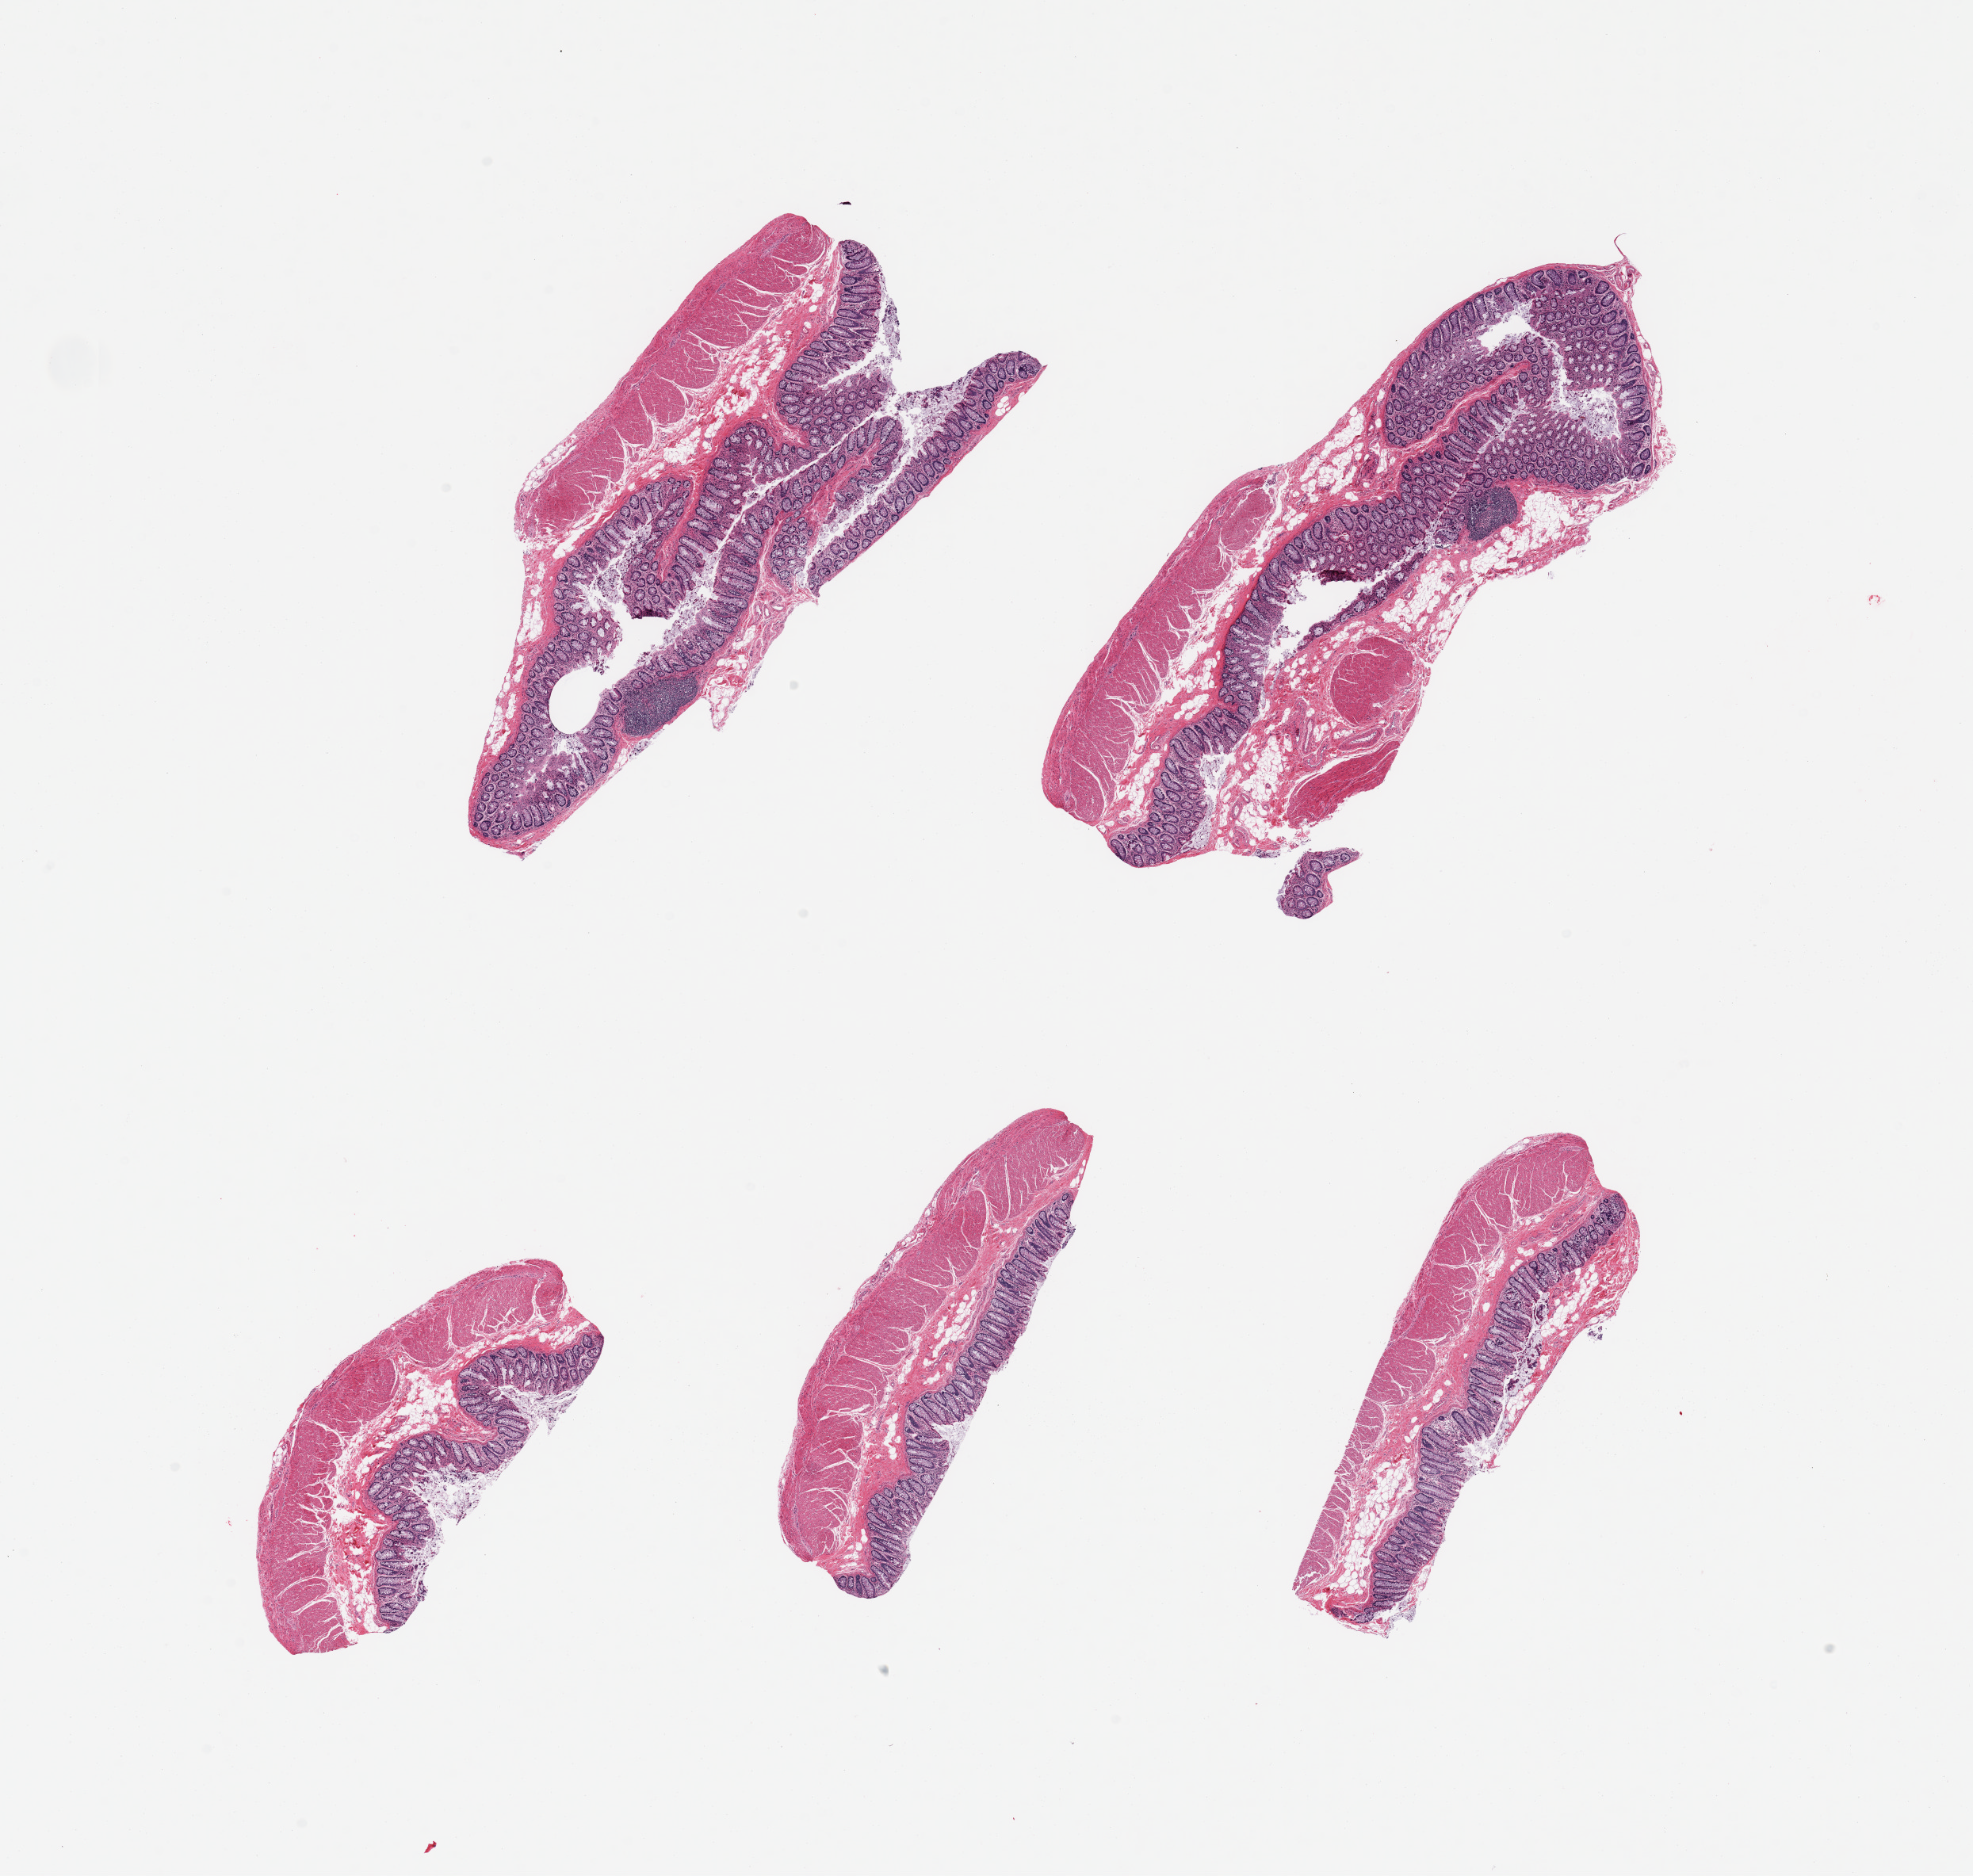
Whole-slide image, H&E stain, brightfield, shown as a low-resolution overview of the whole scanned area (about 19.7 x 18.7 mm), PAXgene-fixed paraffin-embedded (PFPE) section, target tissue: transverse colon, donor tissue sample. Male donor.
Reviewer comment on this tissue sample: 5 pieces; well dissected full thickness.